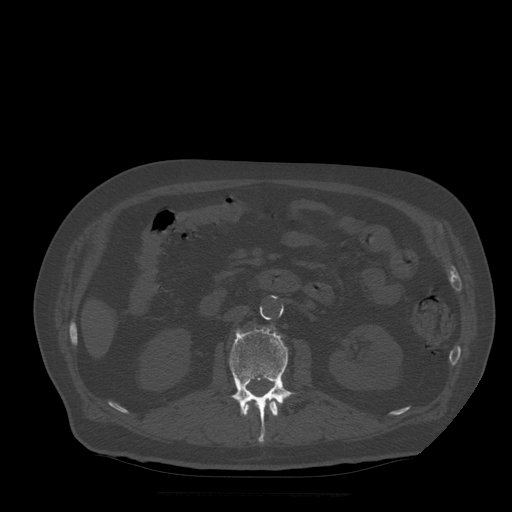
CT including the spine, one axial slice; position 169 of 522 along the scan axis; bone window (W 1800 / L 400 HU); 1.25 mm slice thickness; 512 × 512 image matrix, field of view 420 × 420 mm. Patient age 72 years. Case-level facts recorded for this patient, not image findings: primary cancer: prostate.
Structures marked on this image (semi-automatic segmentation, software-assisted and operator-edited):
- L1 vertebra: bounding box [x1, y1, x2, y2] px = [245, 398, 278, 417]
- L2 vertebra: [230, 329, 297, 443]